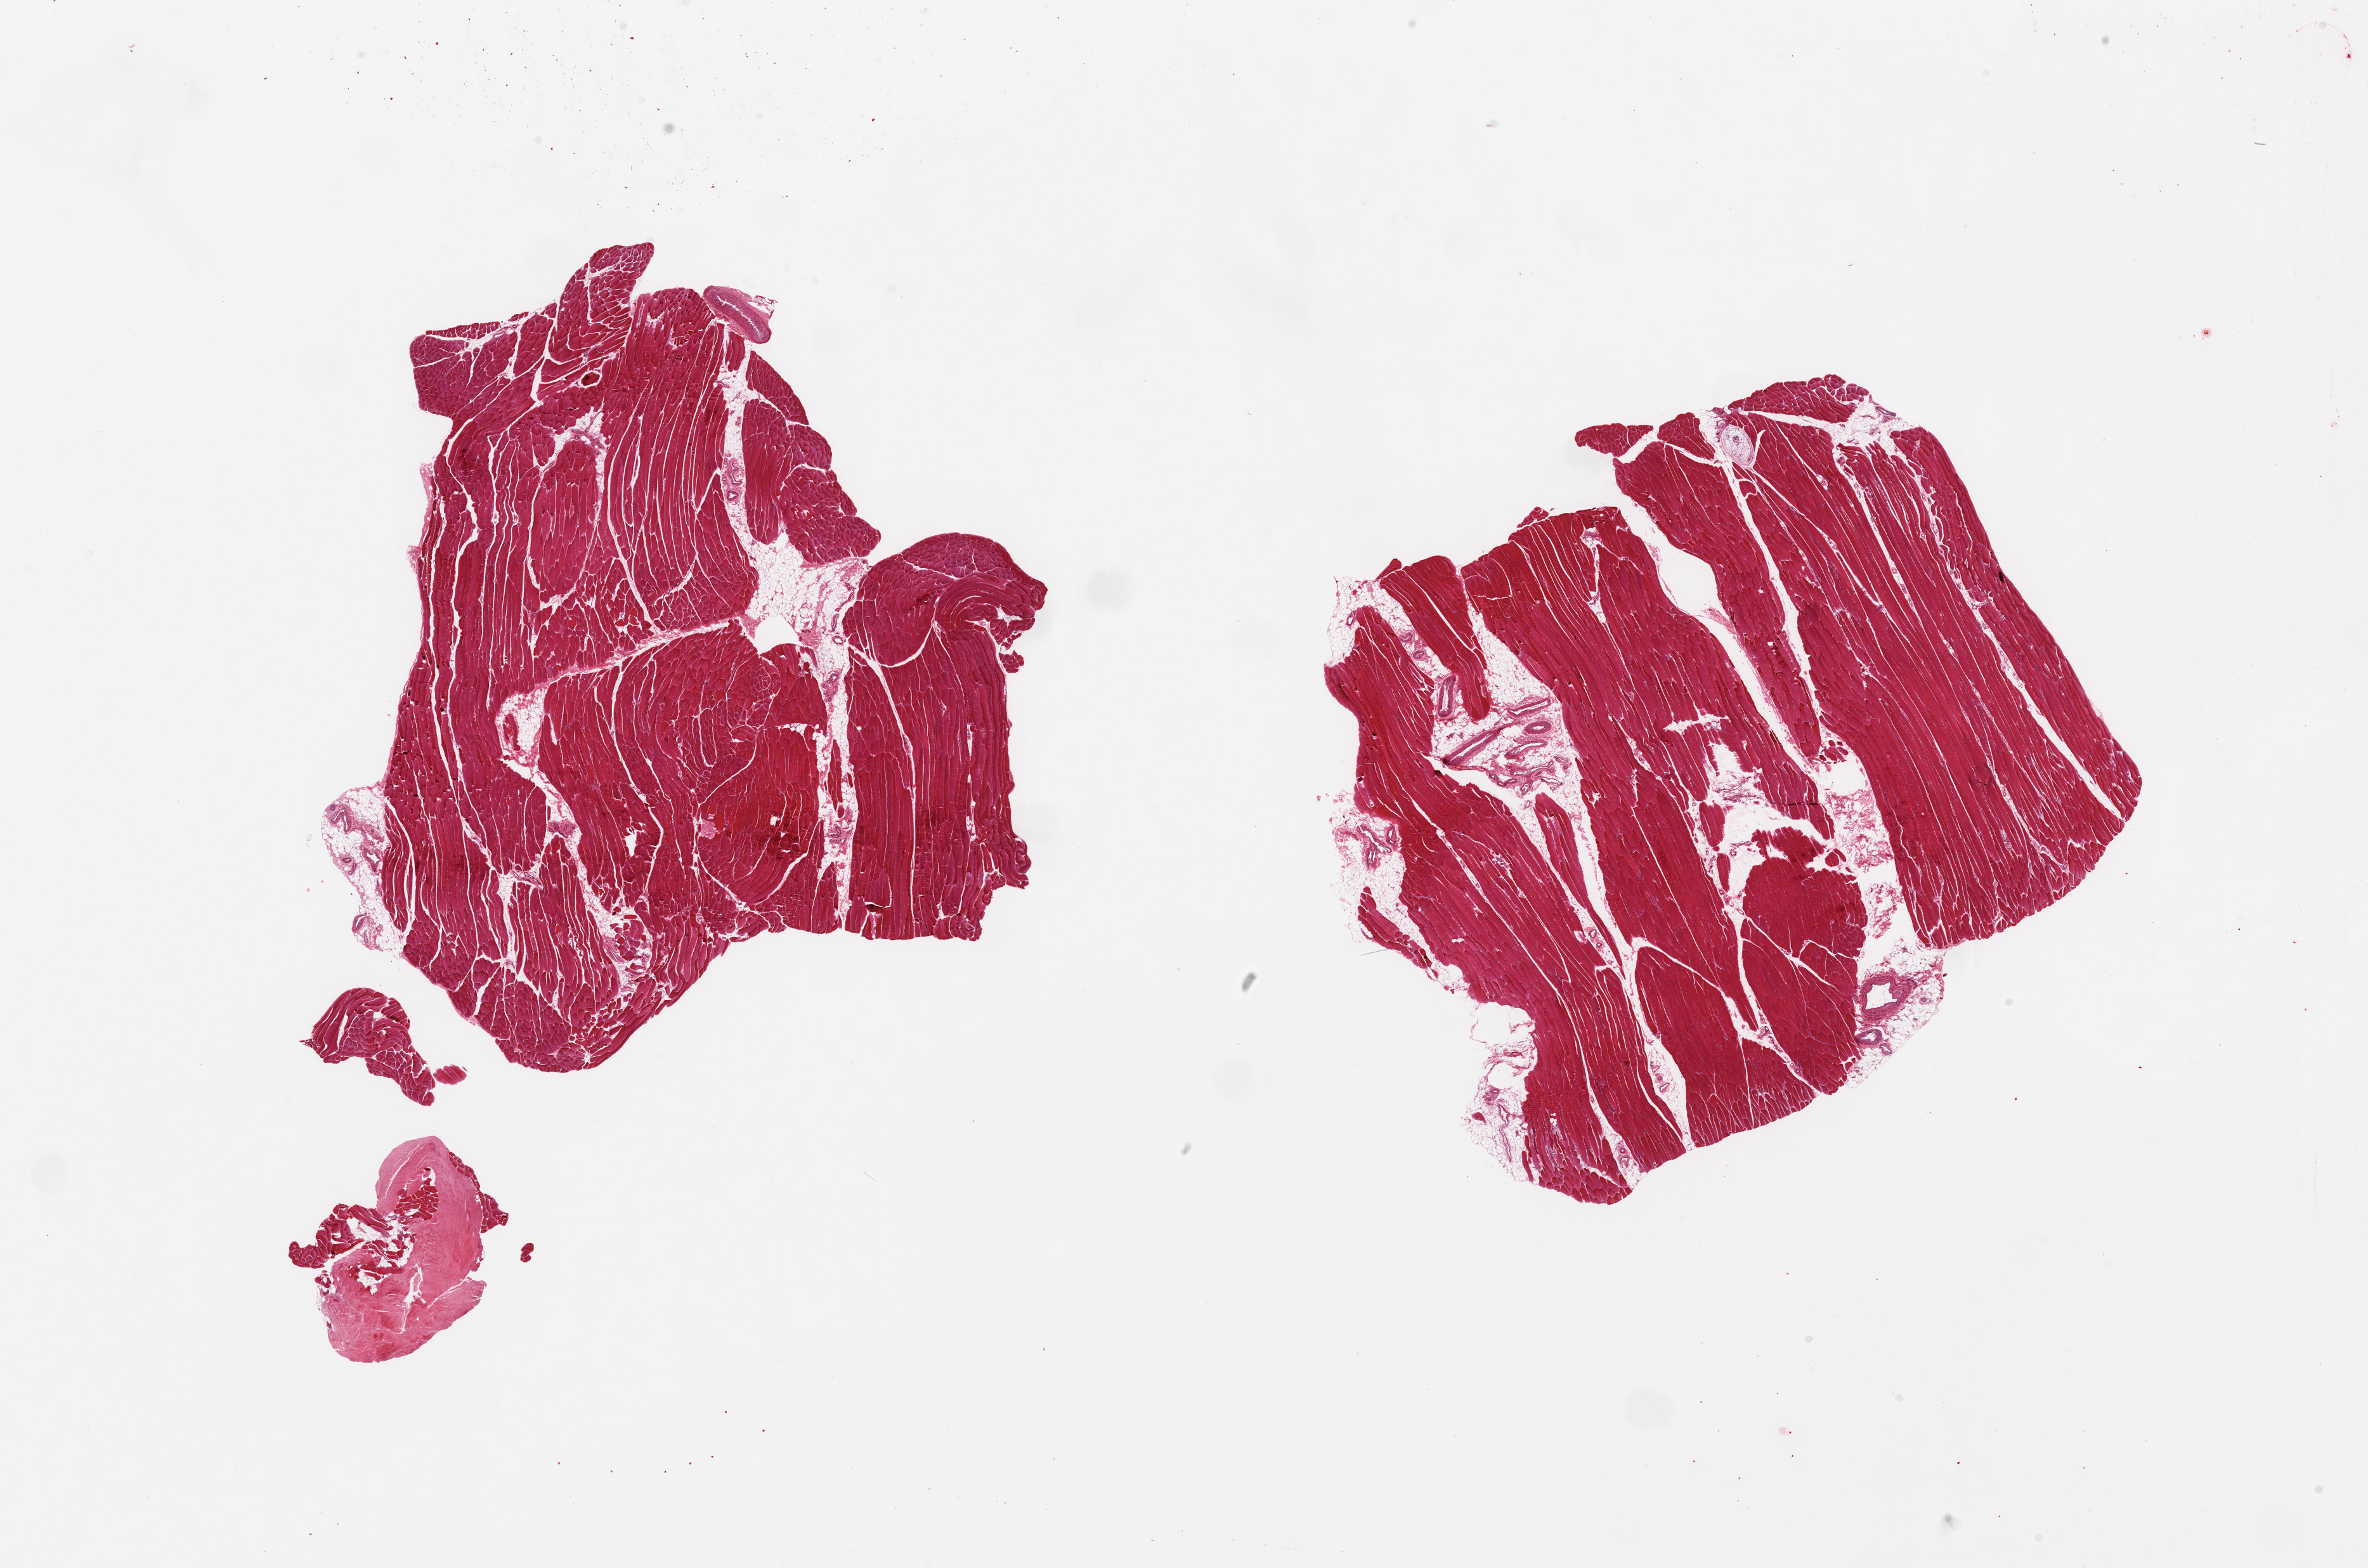
Digitized haematoxylin and eosin-stained section, brightfield, low-resolution overview of the scanned area, about 29.5 x 19.6 mm (acquisition: 20x scan), PAXgene-fixed, paraffin-embedded tissue, target tissue: skeletal muscle, donor tissue sample. Male donor.
Pathologist's review note for this sample: 2 pieces; includes ~10-15% internal and external fat/vessels, Pacinian corpuscle and detached fragment of tendon.